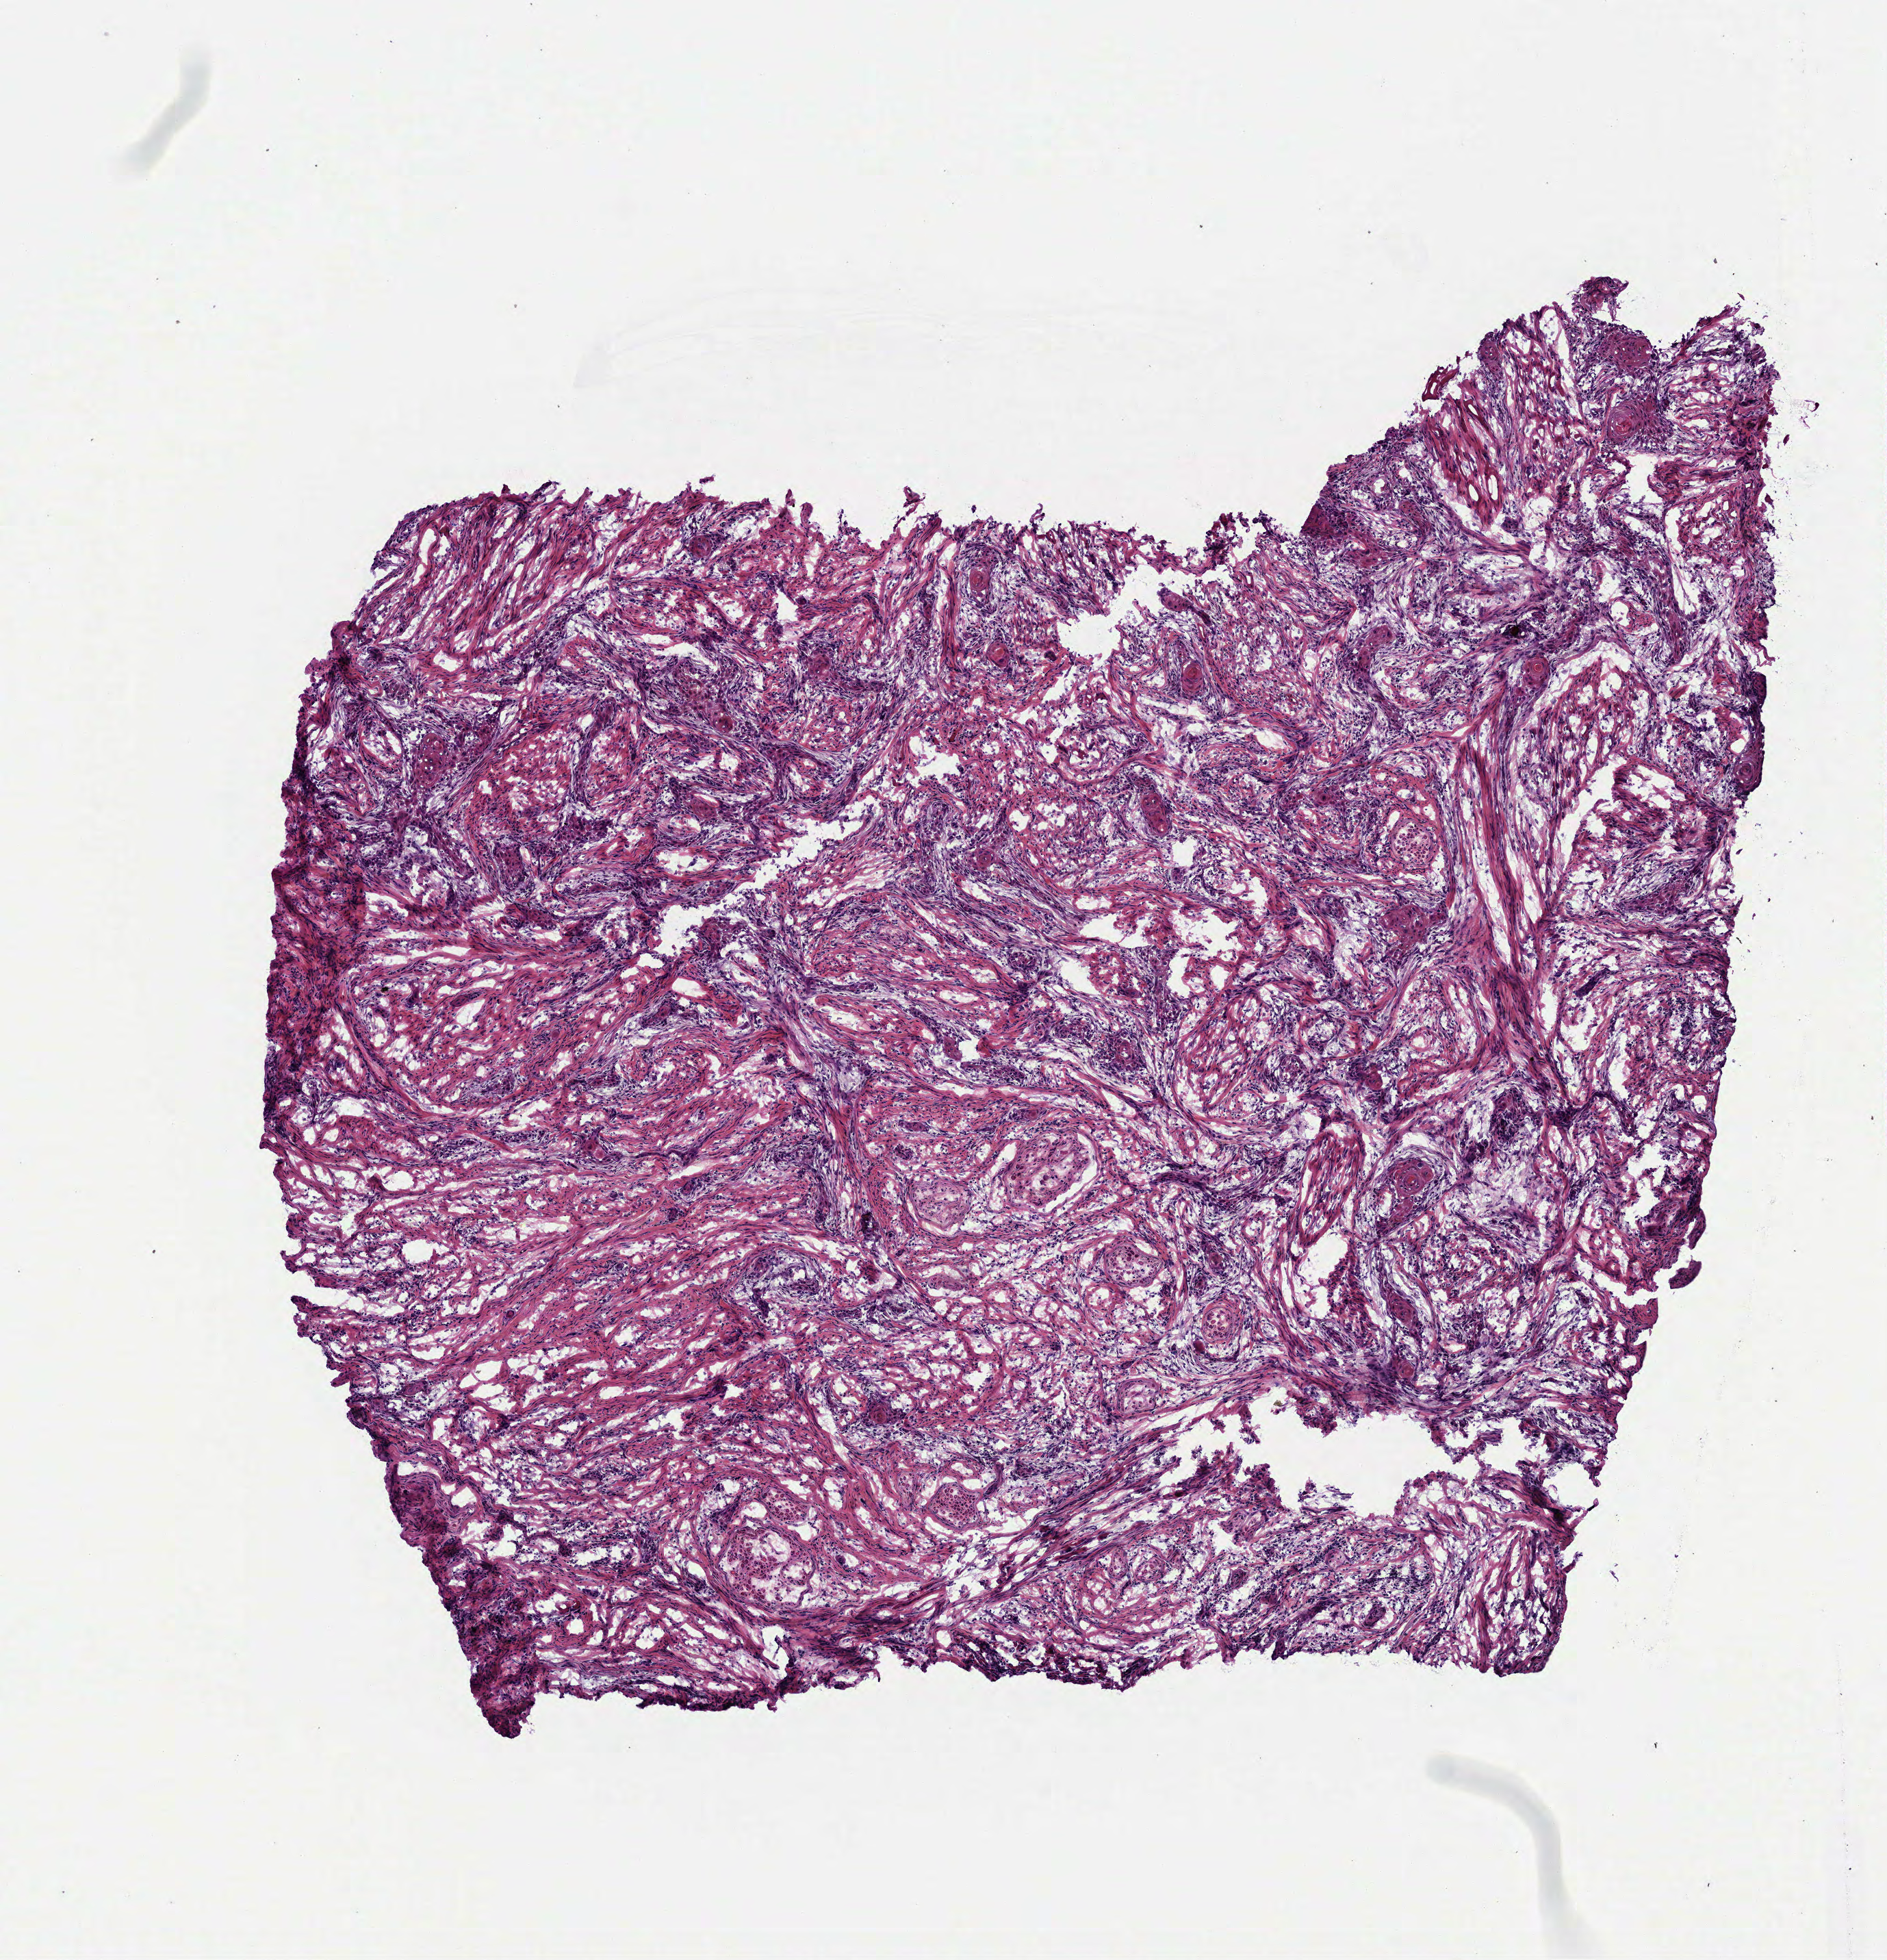
H&E-stained whole-slide image — whole scanned area (about 5.6 x 5.8 mm) shown as a low-resolution overview. Frozen section from the bottom of the tissue portion. Primary tumour sample from the head and neck. Male, age 64 years at initial diagnosis. Histologic grade: G2 (moderately differentiated). Pathologist review of this section (percent, as recorded): tumour cells 75%, tumour nuclei 65%, normal cells 0%, stromal cells 25%, necrosis 0%.
Lymph nodes positive (case pathology): 1 of 75 examined. Diagnosis: Squamous cell carcinoma, NOS (tongue, NOS). AJCC pathologic stage: IVA (7th edition).